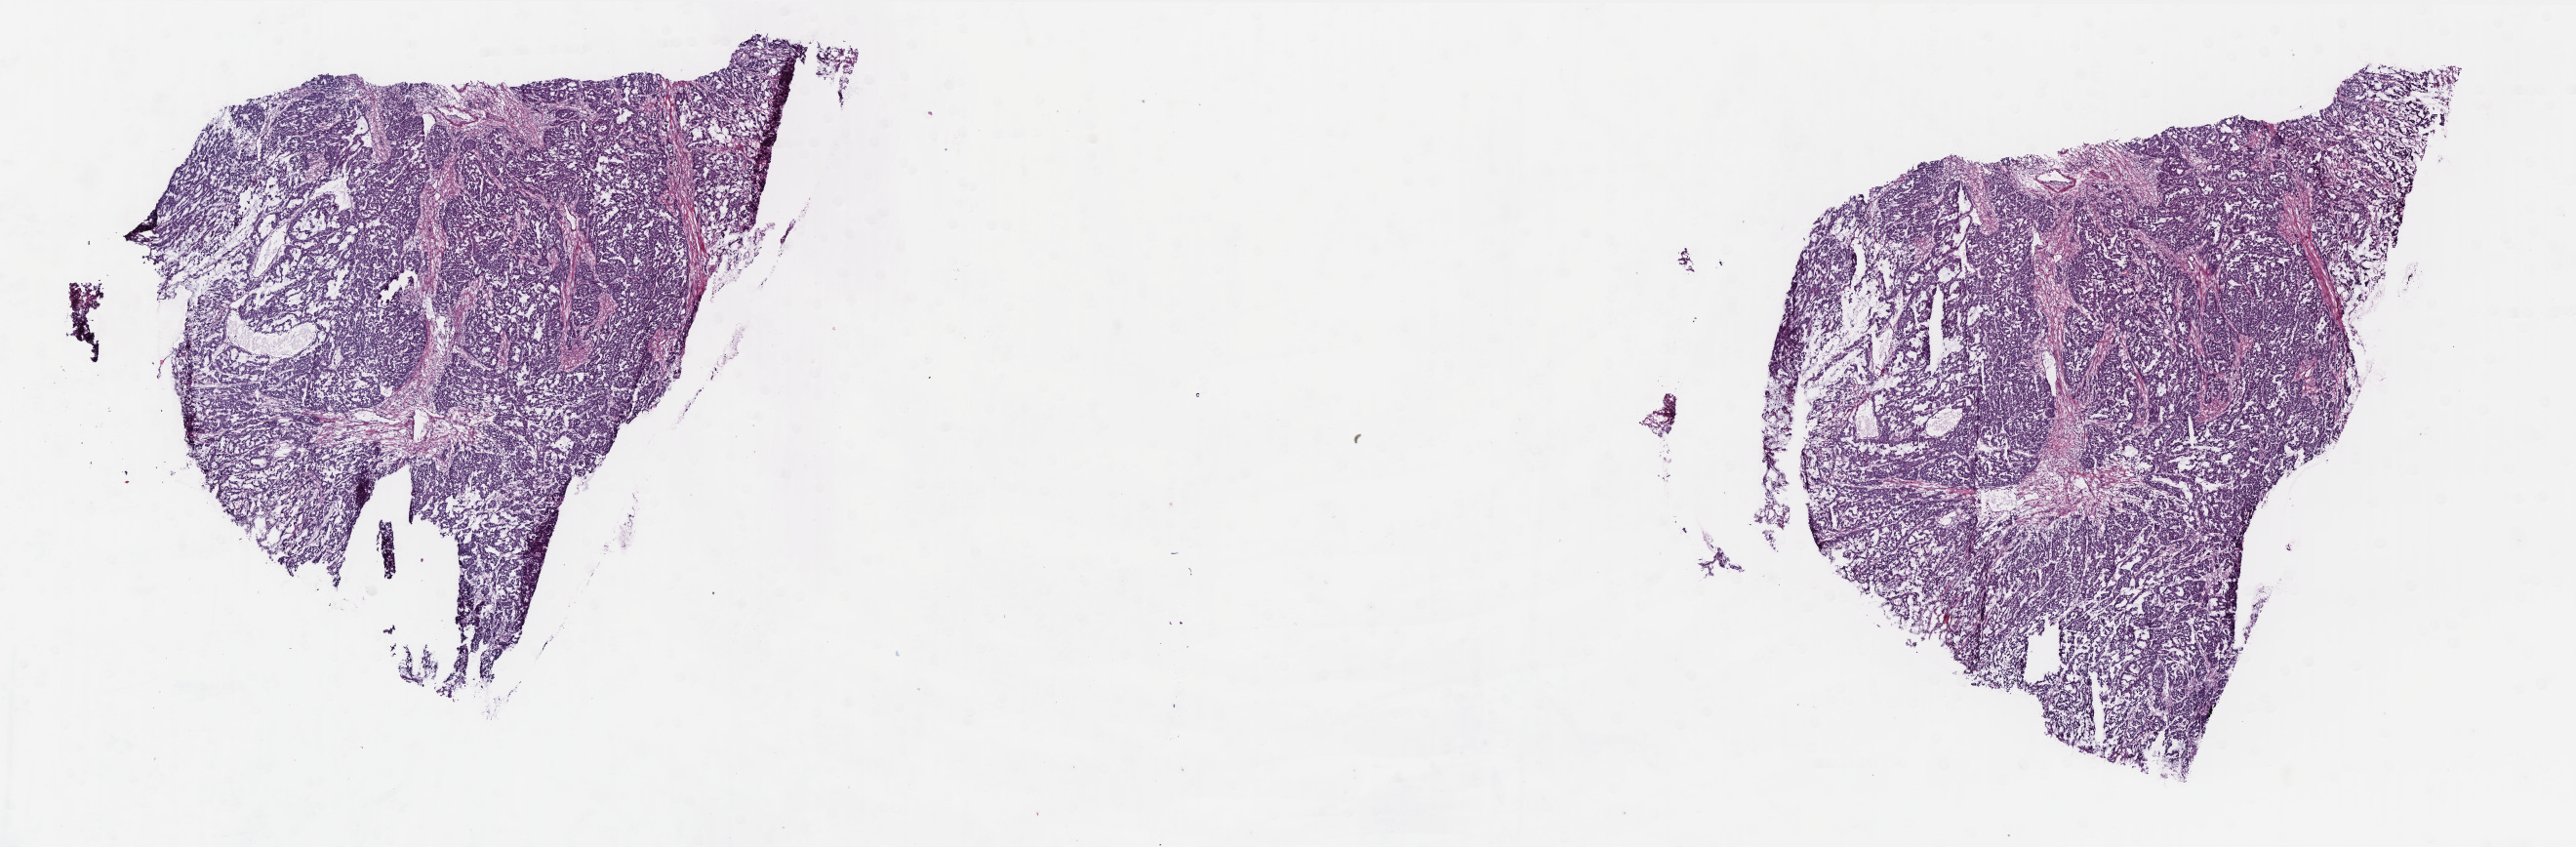
Hematoxylin and eosin (H&E) stained whole-slide image, whole scanned area (about 21.2 x 7.0 mm, acquisition: 40x scan) shown as a low-resolution overview; frozen section; sample: primary tumour, colon. Male patient; age at initial diagnosis 80 years. Composition of this section per pathologist review: tumour cells 90%, tumour nuclei 90%, normal cells 0%, stromal cells 9%, necrosis 1%. Infiltration values recorded for this section: lymphocyte infiltration 2%, monocyte infiltration 1%, neutrophil infiltration 2%.
Pathologic diagnosis: Mucinous adenocarcinoma (ascending colon). AJCC pathologic stage: IIIB. Lymph nodes positive (case pathology): 2 of 24 examined.